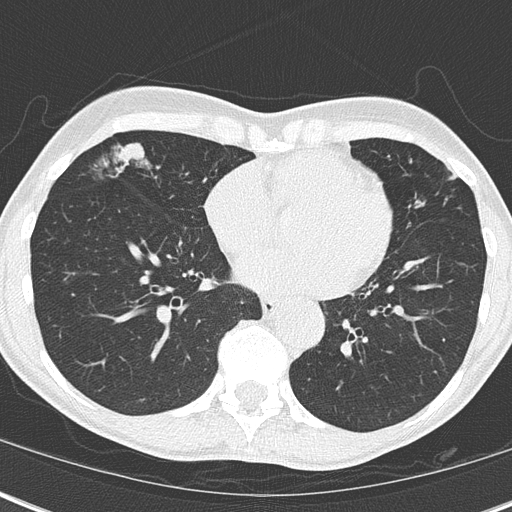
Low-dose screening chest CT, axial slice, third screening round (two years after baseline), lung window (W 1500 / L -600 HU), 2 mm slice thickness, slice 107 of 173 in the series. Female, age 67 years at enrolment. Current smoker at enrolment.
- Expert reader's lesion annotation, bounding box (x1, y1, x2, y2) in pixels: (91, 136, 186, 213).
- The exam's reader record, not a measurement of the box and not confirmed to be the same lesion: non-calcified nodule or mass ≥4 mm, right middle lobe, 32 × 17 mm, mixed attenuation, pre-existing on the prior screen: yes; interval growth: yes.
- Participant outcome: lung cancer diagnosed 76 days after this screen — bronchiolo-alveolar adenocarcinoma, NOS, right middle lobe, well differentiated (G1), stage IA (AJCC 6th edition), 25 mm at pathology.